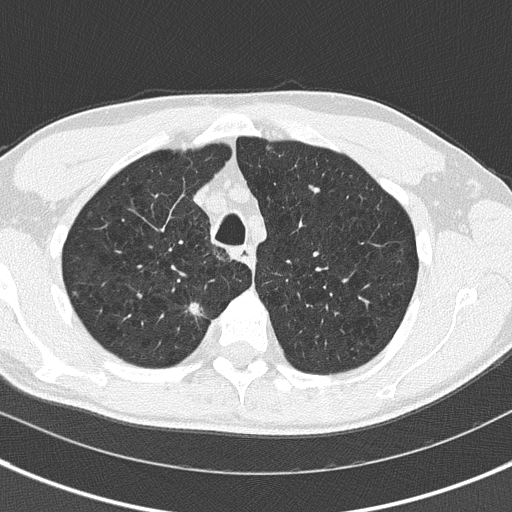
Low-dose screening chest CT, axial slice, first (baseline) screen, lung window (W 1500 / L -600 HU), 2 mm slice thickness, lung (sharp) reconstruction kernel (B50f), slice 38 of 175 in the series. Male participant, aged 56 years at enrolment. Current smoker at enrolment.
Expert reader's lesion annotation, bounding box (x1, y1, x2, y2) in pixels: (178, 294, 221, 337). The screening reader recorded 3 non-calcified nodules or masses ≥4 mm on this exam (right upper lobe, right upper lobe, left lower lobe); which of them this box marks is not recorded. Official screen result: positive, change unspecified: nodule(s) >= 4 mm or enlarging nodule(s), mass(es), or other non-specific abnormalities suspicious for lung cancer. Later outcome: lung cancer diagnosed 228 days after this screen — non-small cell carcinoma, right upper lobe, stage IIIA (AJCC 6th edition), 21 mm at pathology.